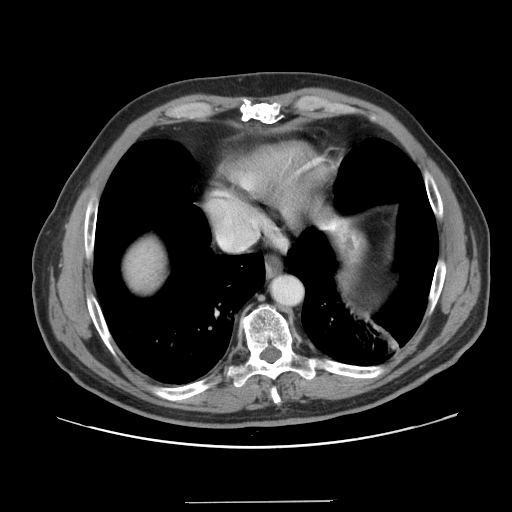
Contrast-enhanced abdominal CT, one axial slice; slice 145 of 151 in the series (ordered by position); 120 kVp; intravenous contrast given; soft-tissue window (W 400 / L 40 HU); 512 × 512 image matrix. Male patient, age 63 years. Case-level facts recorded for this patient, not image findings: diagnosis: colorectal cancer liver metastases, imaged before liver resection; multiple liver metastases: no.
Outlined on this slice (outlined manually by an expert reader):
- hepatic veins: box from (x=219, y=238) to (x=245, y=249) px
- liver: (x=123, y=235)–(x=167, y=294)
- planned liver remnant (the part of the liver to remain after resection): (x=123, y=235)–(x=167, y=295)